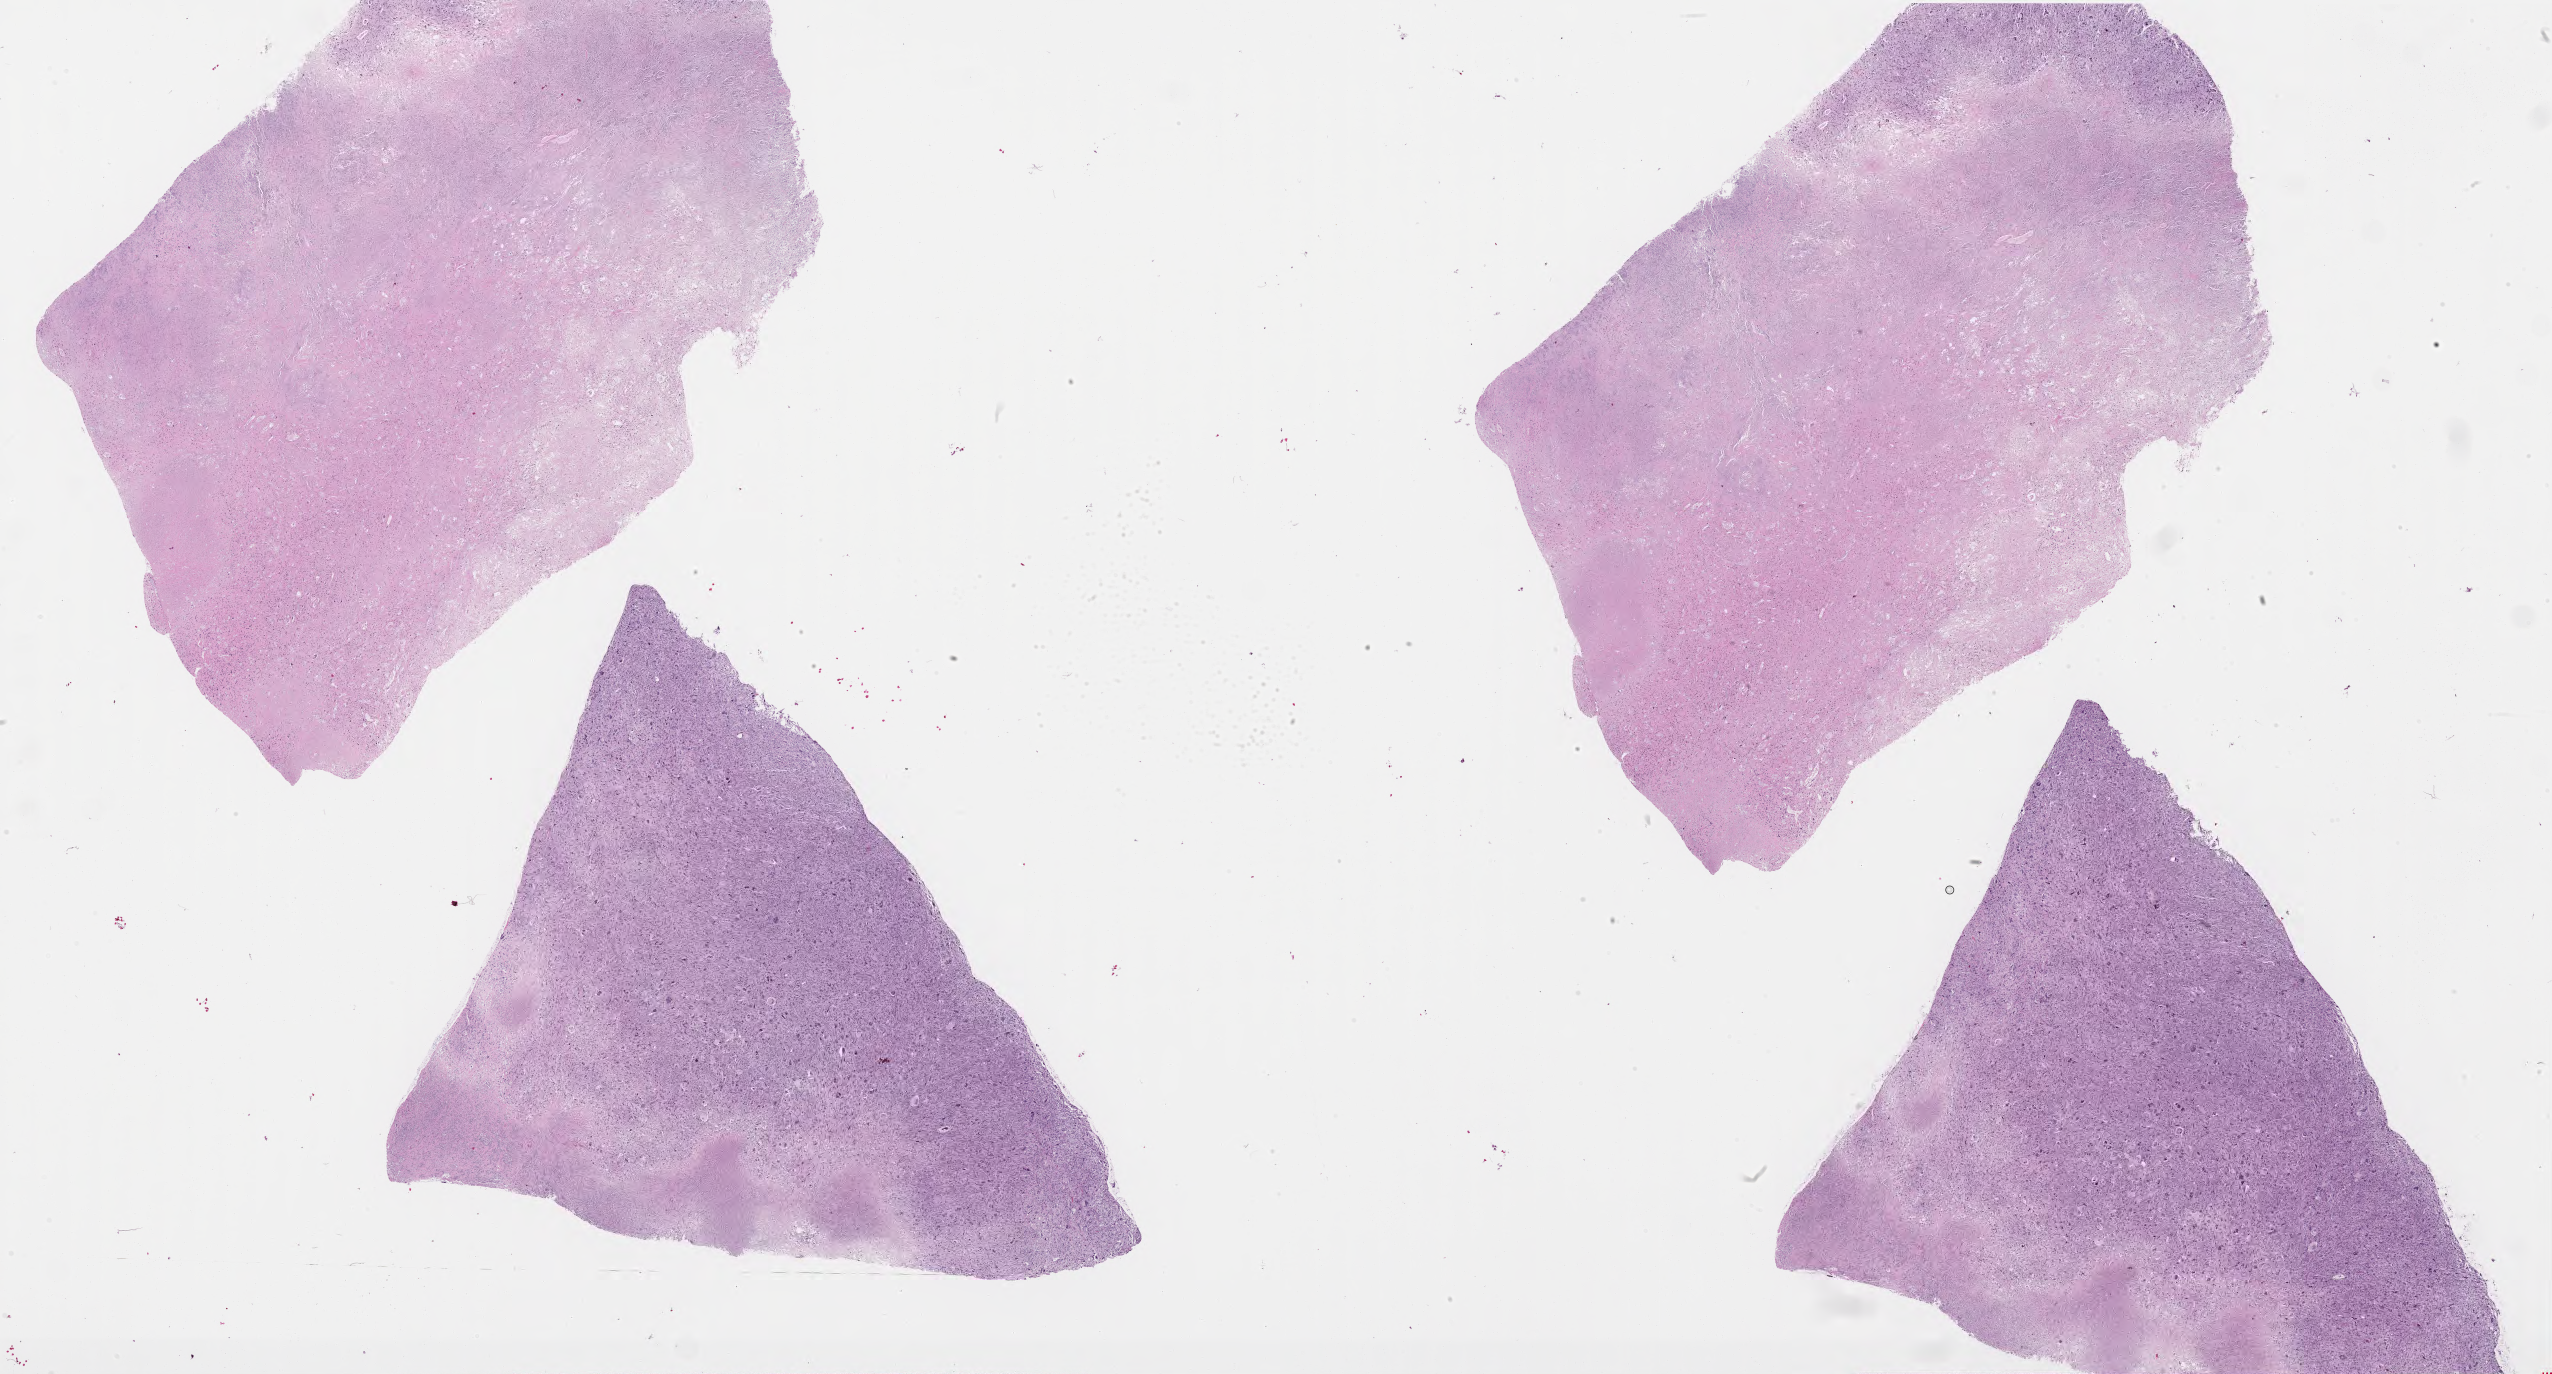
Whole-slide histology image, H&E, whole scanned area (about 41.0 x 22.1 mm, from a 40x scan) shown as a low-resolution overview; formalin-fixed paraffin-embedded (FFPE) diagnostic section; primary tumour sample from the connective, subcutaneous and other soft tissues. Male, age 71 years at initial diagnosis.
Diagnosis: Undifferentiated sarcoma.